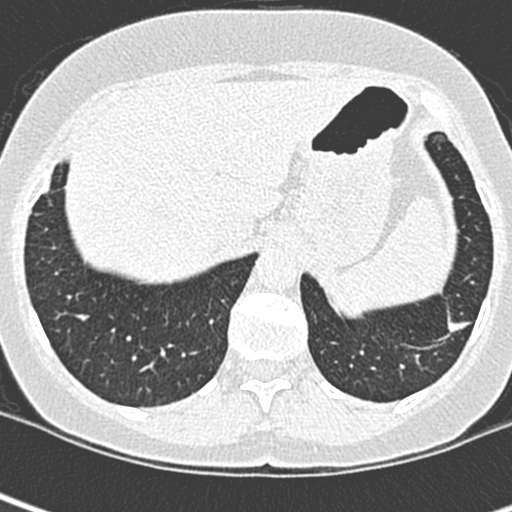
Low-dose screening chest CT, one axial slice. Slice 53 of 252 in the series (ordered by position). 120 kVp. Lung window (W 1500 / L -600 HU). 512 × 512 image matrix, field of view 271 × 271 mm.
Structures marked on this image (expert manual segmentation):
- lesion 1 (tumor, lower lobe of left lung): box from (x=447, y=319) to (x=471, y=335) px